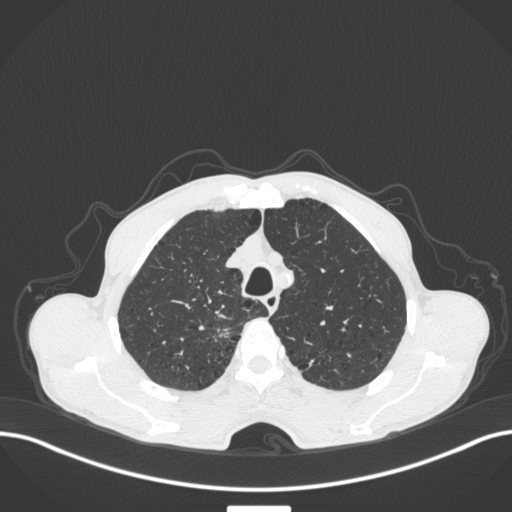
Chest CT, one axial slice; position 341 of 445 along the scan axis; reconstruction kernel B31f; 120 kVp; lung window (W 1500 / L -600 HU); 1 mm slice thickness; 512 × 512 image matrix. Male patient, age 70 years. From the clinical record (not read from this slice): clinical TNM (as recorded): T1a N0 M0.
Annotated regions visible in this slice (rectangle marked by the reading radiologist):
- lung tumour (recorded histology: adenocarcinoma): box from (x=209, y=318) to (x=241, y=343) px